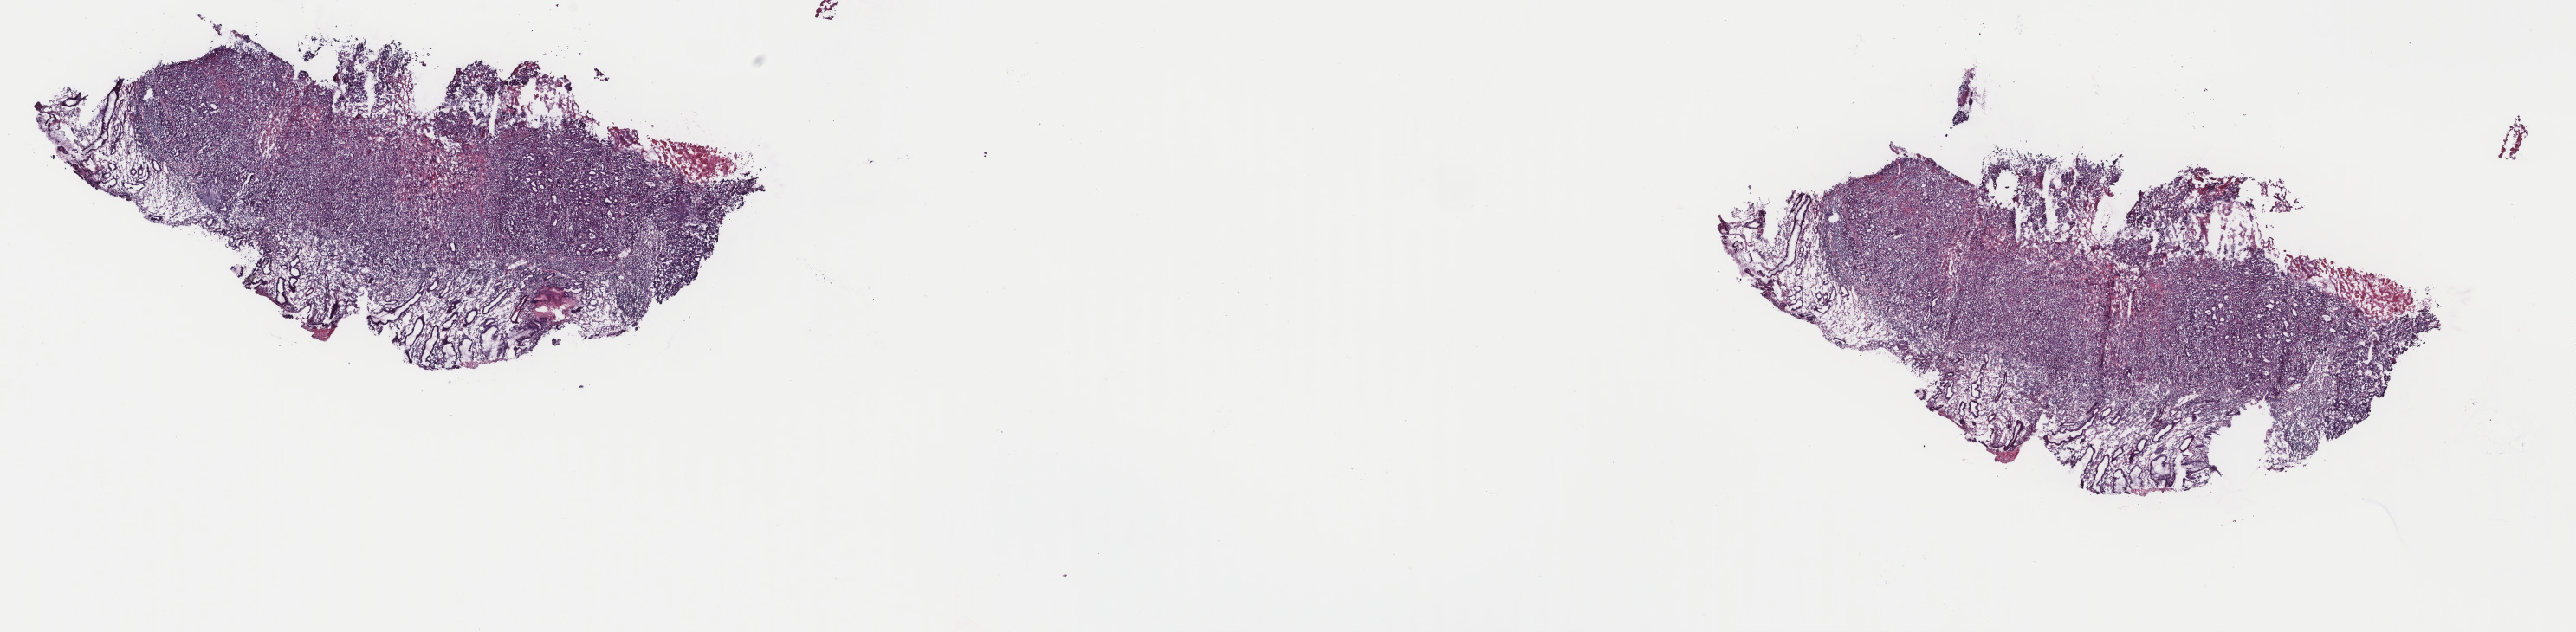
Hematoxylin and eosin (H&E) stained whole-slide image — low-resolution overview of the scanned area, about 23.6 x 5.8 mm, frozen section from the top of the tissue portion, primary tumour sample from the stomach. Female patient; age at initial diagnosis 56 years. Histologic grade: G3 (poorly differentiated). Pathologist review of this section (percent, as recorded): tumour cells 38%, tumour nuclei 75%, normal cells 25%, stromal cells 22%, necrosis 15%. Infiltration values recorded for this section: lymphocyte infiltration 15%, monocyte infiltration 0%, neutrophil infiltration 0%.
Diagnosis: Carcinoma, diffuse type (body of stomach). AJCC pathologic stage: IIIC (7th edition).